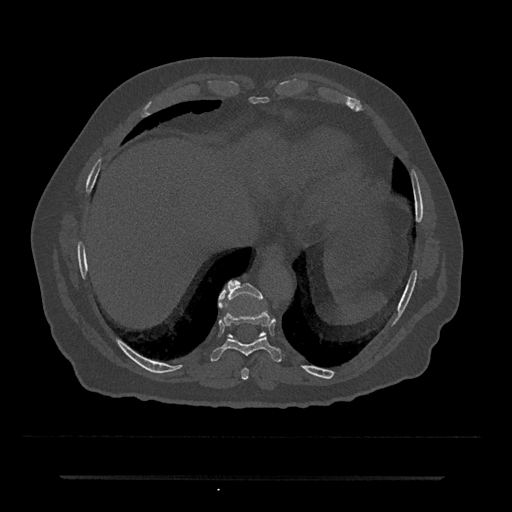
CT including the spine, one axial slice. Position 271 of 797 along the scan axis. 120 kVp. Bone window (W 1800 / L 400 HU). 512 × 512 image matrix, field of view 437 × 437 mm. Male patient, age 69 years. From the clinical record (not read from this slice): primary cancer: prostate.
Annotated regions visible in this slice (semi-automatic segmentation, software-assisted and operator-edited):
- T10 vertebra: bounding box <219,280,266,338> (left, top, right, bottom; pixels)
- T8 vertebra: <241,368,249,380>
- T9 vertebra: <210,290,283,362>